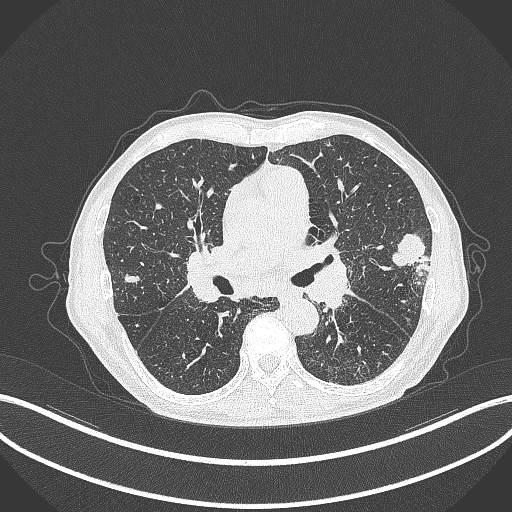
Chest CT, one axial slice. Position 227 of 463 along the scan axis. Lung window (W 1500 / L -600 HU). 512 × 512 image matrix, field of view 400 × 400 mm. Male patient, age 74 years. From the clinical record (not read from this slice): clinical TNM (as recorded): T2a N1 M0.
Annotated regions visible in this slice (rectangle marked by the reading radiologist):
- lung tumour (recorded histology: adenocarcinoma): box from (x=386, y=228) to (x=430, y=275) px